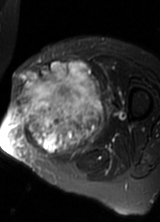
MRI of an extremity soft-tissue mass, one axial slice; position 35 of 69 along the scan axis; T2-weighted fat-saturated; MR volume resampled by the dataset authors to the PET/CT grid (not the native acquisition matrix); 160 × 222 image matrix, field of view 156 × 217 mm. Female patient. From the clinical record (not read from this slice): histological type: pleomorphic leiomyosarcoma; grade: high; site of the primary tumour: left thigh.
Outlined on this slice (expert contour drawn on MRI and transferred to this co-registered scan by the dataset authors):
- gross tumour volume including surrounding oedema: bounding box (x1, y1, x2, y2) in pixels: (16, 61, 110, 158)
- gross tumour volume (mass): (16, 61, 105, 158)